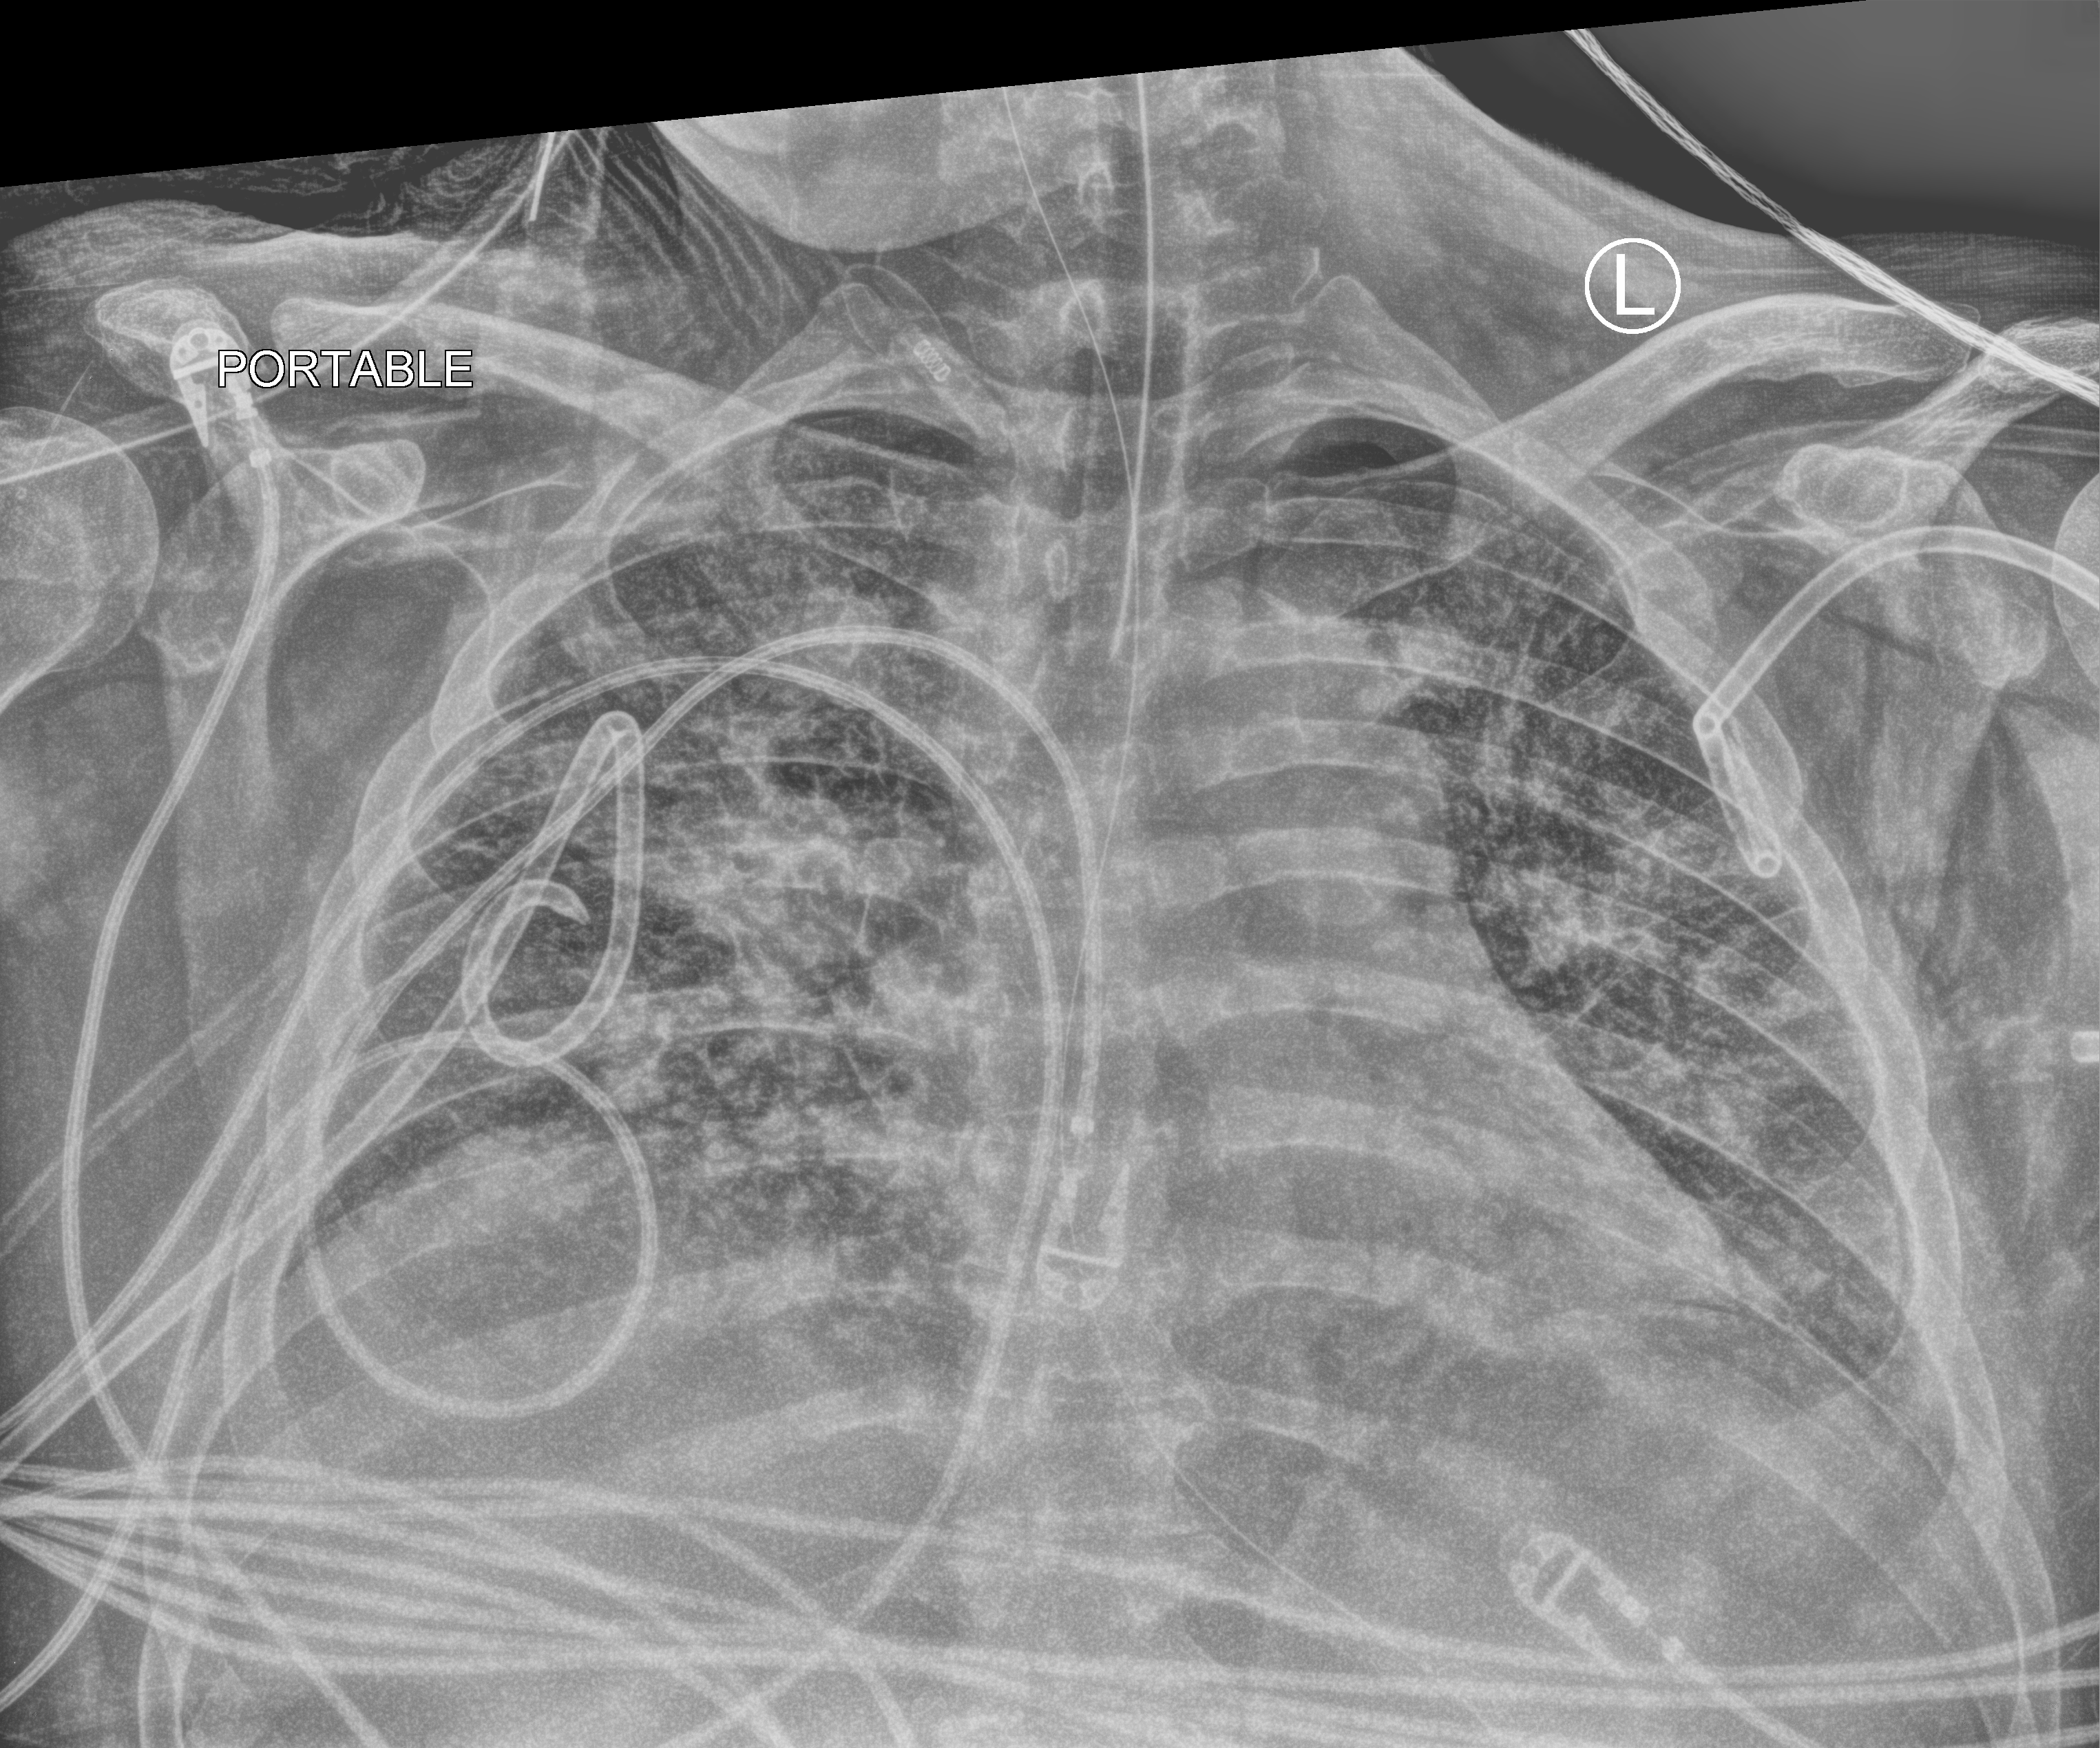
Bedside chest radiograph (computed radiography); anteroposterior (AP) projection. Patient hospitalised with COVID-19, aged 18–59 years.
Admission-level facts for this patient (not findings on this image; timing relative to this image not recorded): mechanically ventilated during this hospital stay: yes.